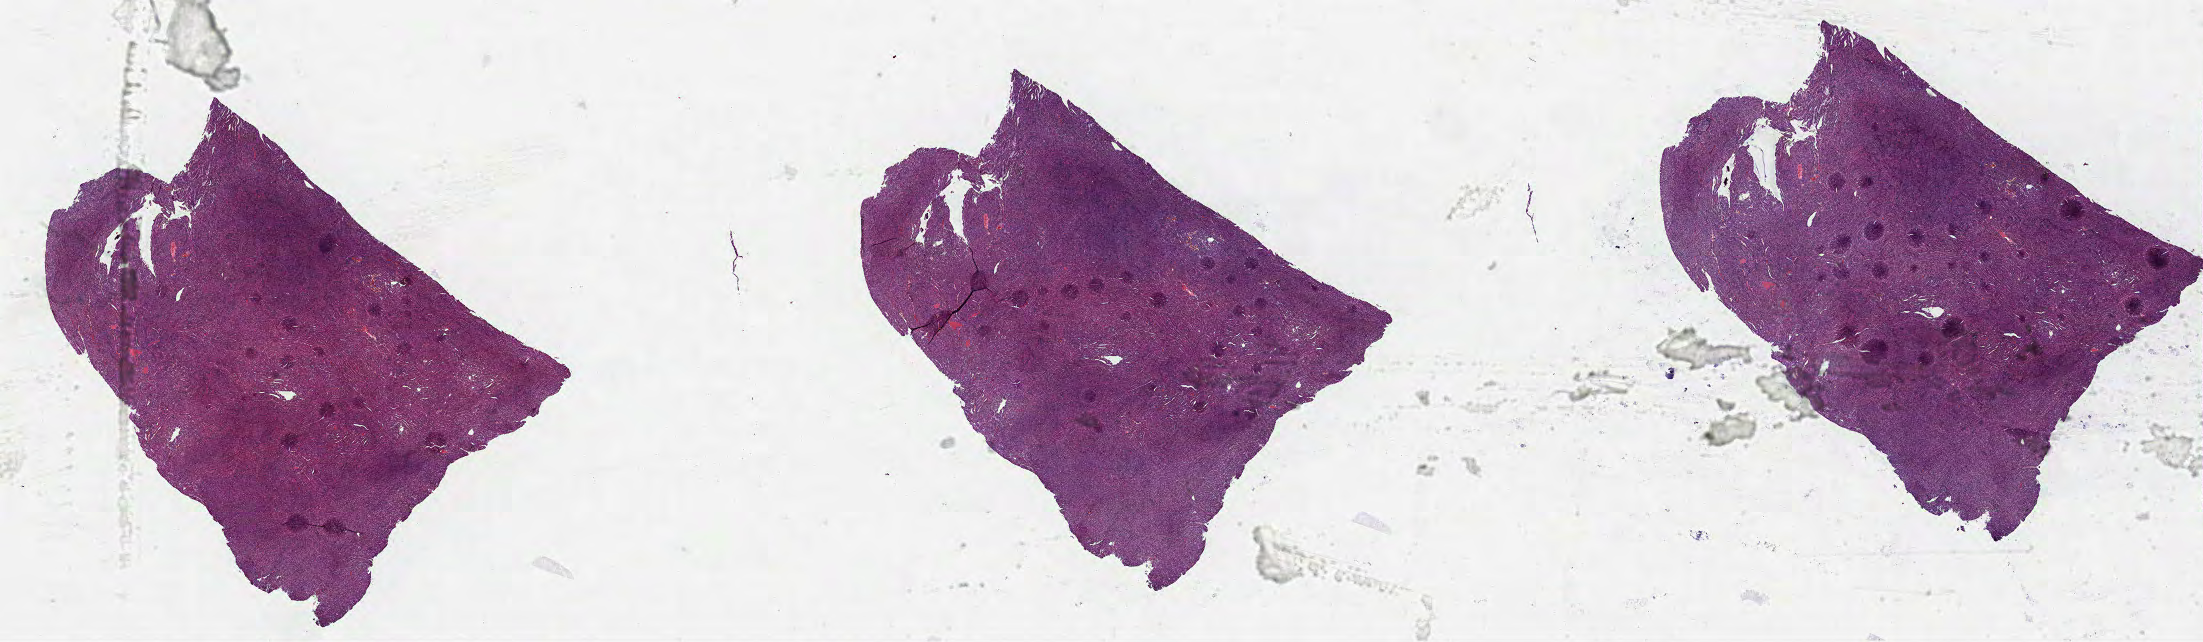
Whole-slide histology image, Hematoxylin and eosin (H&E) stained, shown as a low-resolution overview of the whole scanned area (about 35.5 x 10.4 mm); FFPE section; kidney, primary tumour sample. Female, age 59 years at initial diagnosis.
Laterality: left. Histologic diagnosis: Papillary adenocarcinoma, NOS. AJCC pathologic stage: I. TNM: T1 NX M0.